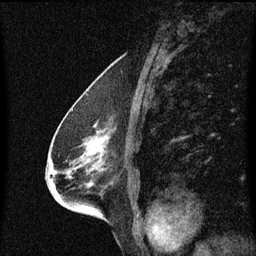
Breast MRI (dynamic contrast-enhanced), one sagittal slice; position 35 of 60 along the scan axis; dynamic contrast-enhanced series, image 2 of 3 at this slice position (ordered by acquisition); 1.5 T; TE 4.2 ms, TR 8.4 ms; 2 mm slice thickness; 256 × 256 image matrix. Female patient, age 68 years. From the clinical record (not read from this slice): setting: breast cancer imaged before/during neoadjuvant chemotherapy; receptor status: triple-negative.
Annotated regions visible in this slice (semi-automatically segmented with operator editing):
- analysis volume of interest (the breast-tissue region the enhancement analysis was run in; not a lesion): bounding box <44,114,132,203> (left, top, right, bottom; pixels)
- tumour enhancement mask (voxels above the 70 % enhancement threshold inside the analysis volume of interest): <50,138,105,175>